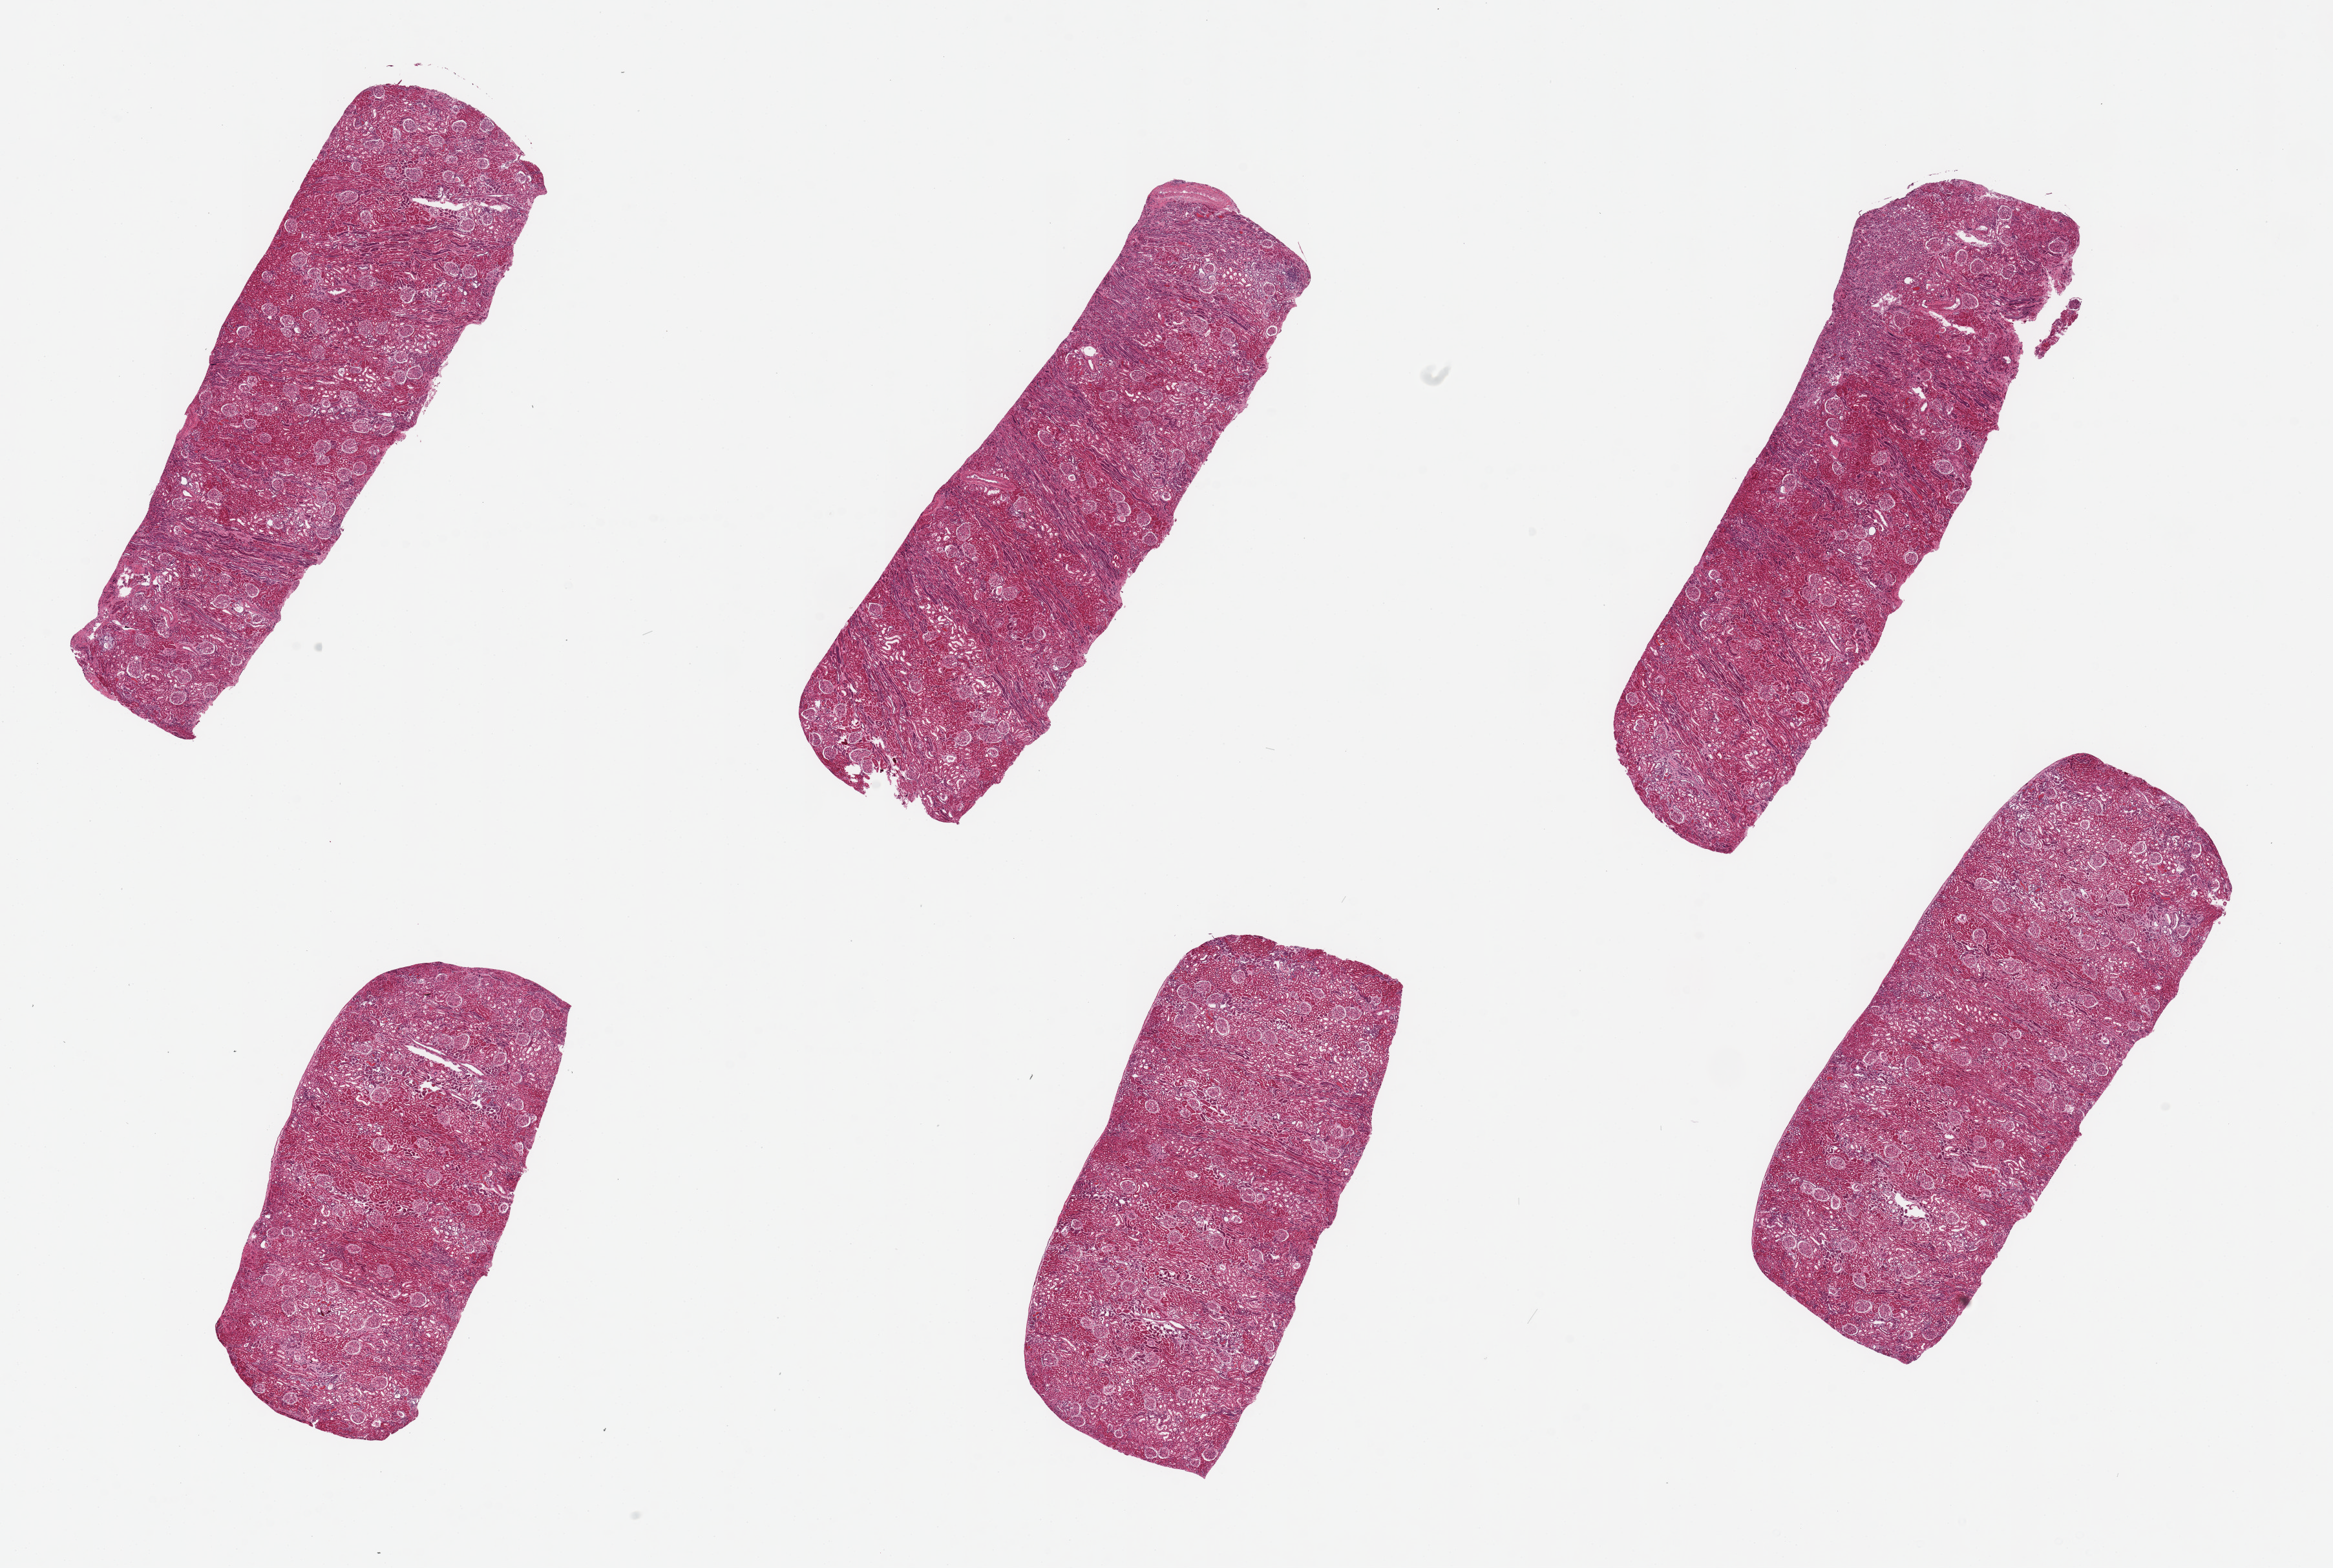
Whole-slide image, hematoxylin and eosin (H&E) stain — a low-resolution overview of the entire scanned area, about 28.5 x 19.2 mm (from a 20x scan). PAXgene-fixed paraffin-embedded (PFPE) section. Target tissue: renal cortex. Tissue donor sample. Donor: female.
Reviewer comment on this tissue sample: 6 pieces, up to 9x3mm; good preservation; no renal lesions.